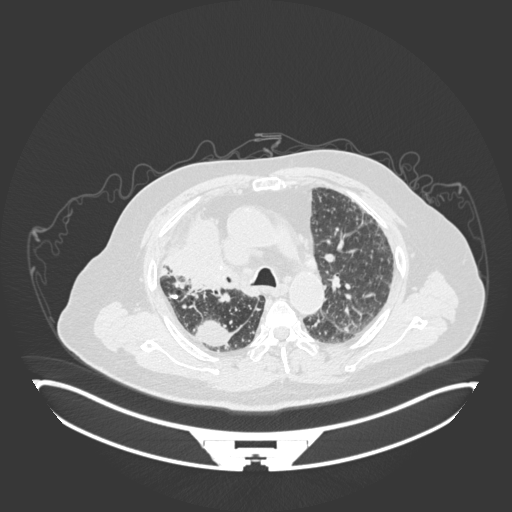
Chest CT, one axial slice; position 124 of 201 along the scan axis; 120 kVp; lung window (W 1500 / L -600 HU); 512 × 512 image matrix, field of view 500 × 500 mm. Male patient, age 69 years. From the clinical record (not read from this slice): clinical TNM (as recorded): T4 N3 M1.
Annotated regions visible in this slice (rectangle marked by the reading radiologist):
- lung tumour (recorded histology: adenocarcinoma): bounding box [x1, y1, x2, y2] px = [158, 211, 236, 297]